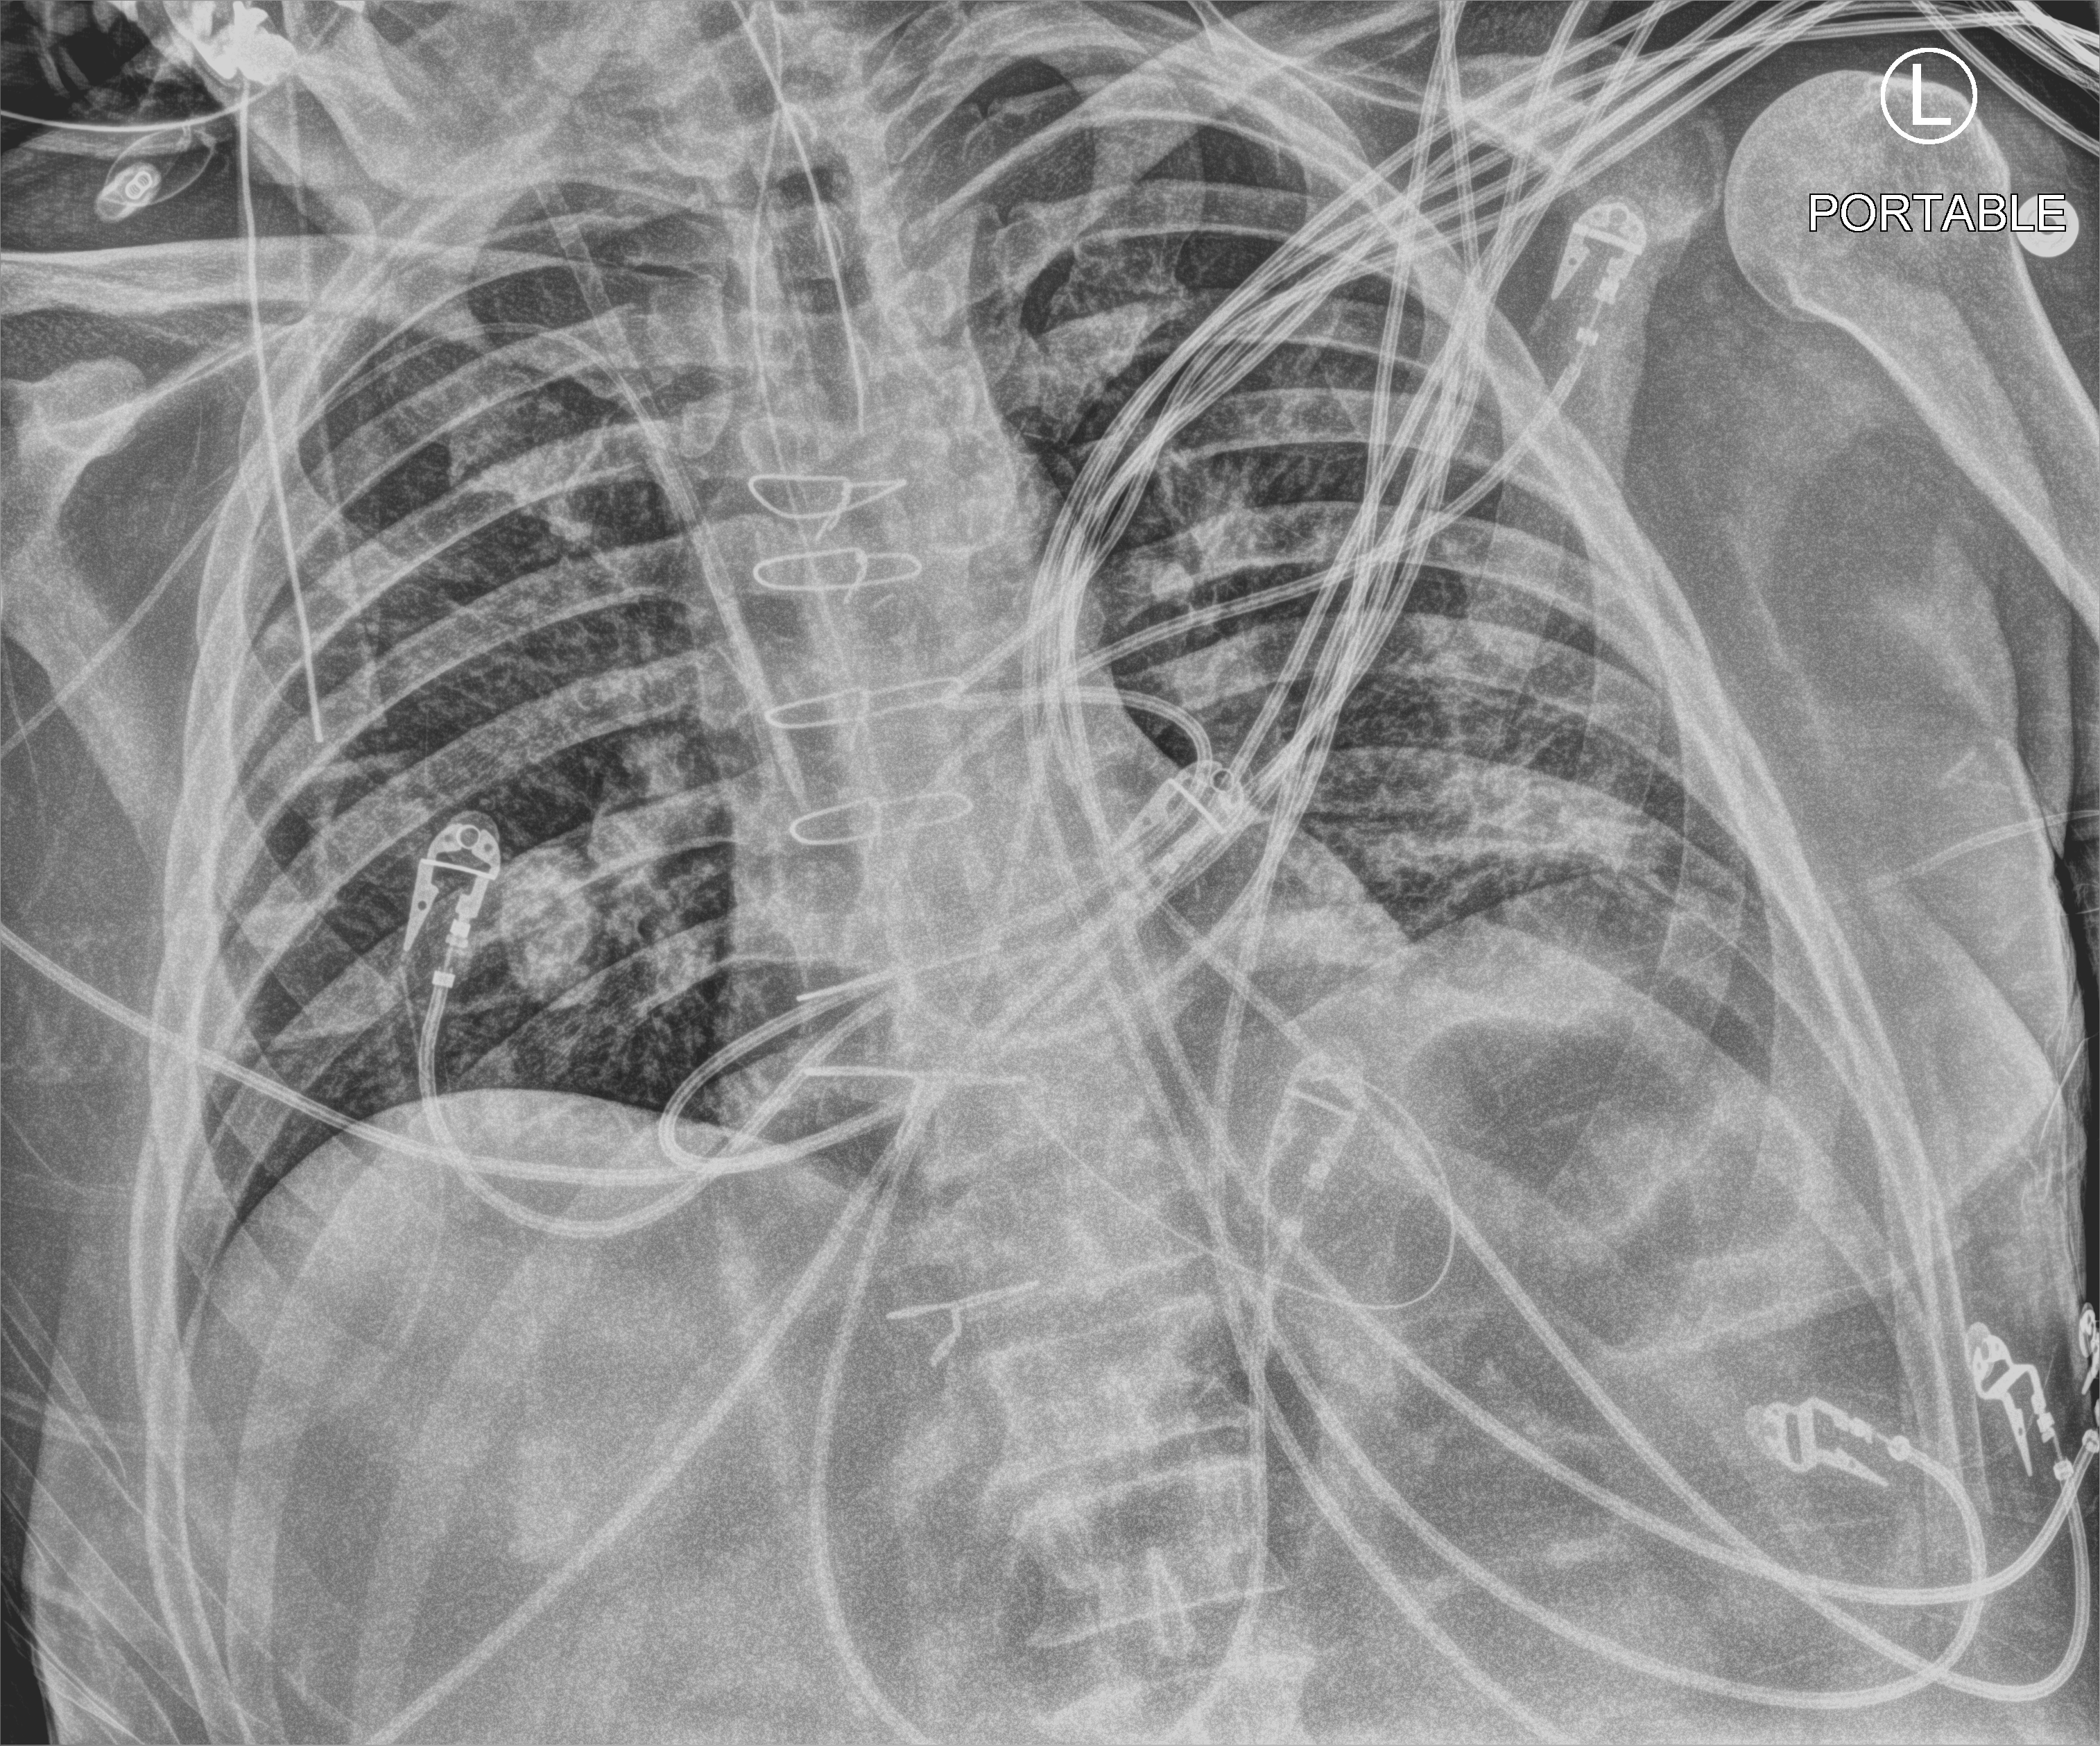
Chest X-ray (portable), anteroposterior (AP) projection. Patient hospitalised with COVID-19; male, aged 60–74 years.
Hospital-stay facts (about this admission, not read from this image; timing relative to this image not recorded):
- mechanically ventilated during this hospital stay: yes
- hypertension (admission record): yes
- admitted to intensive care during this hospital stay: yes